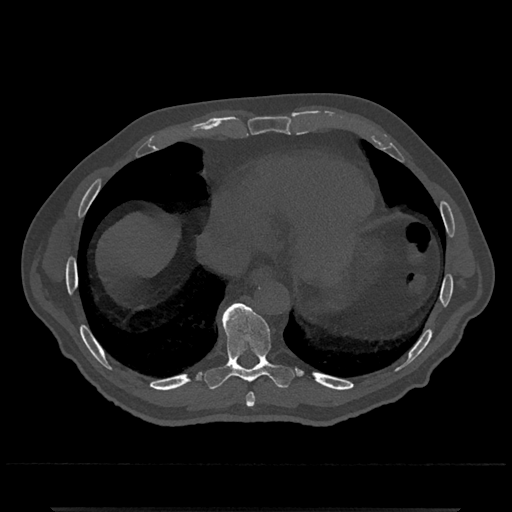
CT including the spine, one axial slice. Slice 616 of 797 in the series (ordered by position). Reconstruction kernel Br40s/3. Bone window (W 1800 / L 400 HU). 0.5 mm slice thickness. 512 × 512 image matrix, field of view 393 × 393 mm. Male patient, age 67 years. Case-level facts recorded for this patient, not image findings: primary cancer: prostate.
Annotated regions visible in this slice (semi-automatically segmented with operator editing):
- T8 vertebra: bounding box <246,393,255,407> (left, top, right, bottom; pixels)
- T9 vertebra: <204,303,295,390>